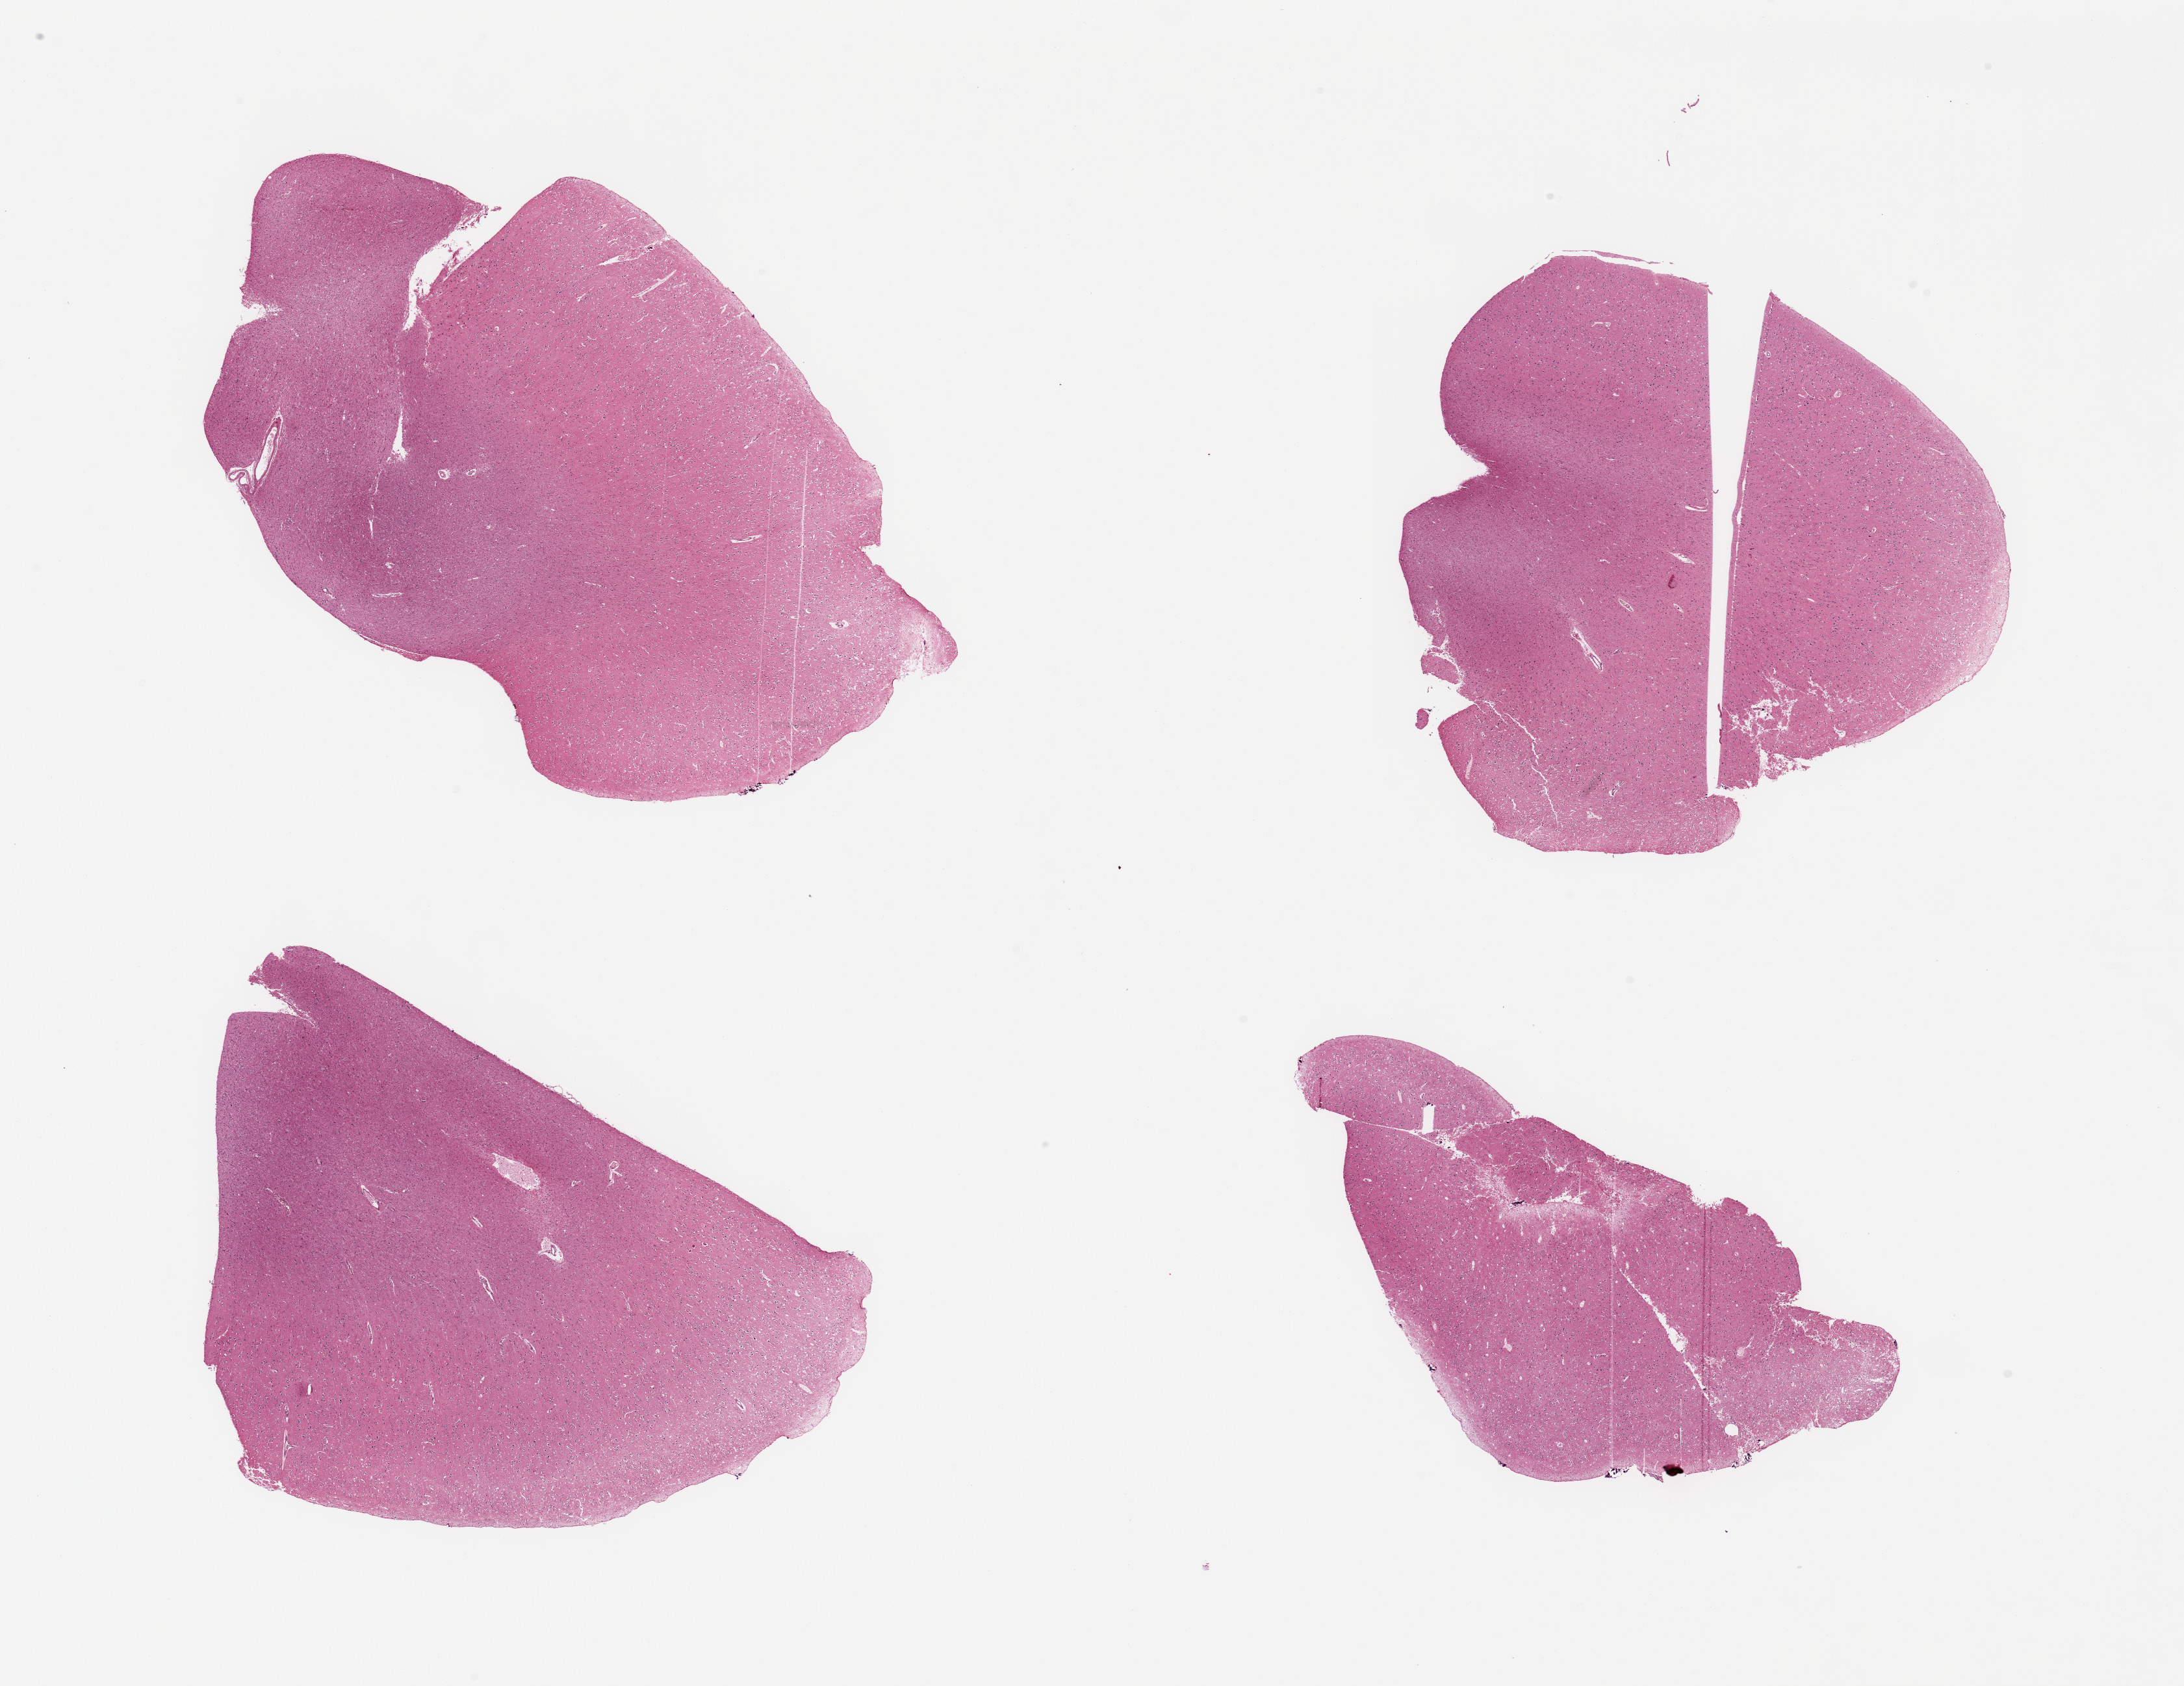
Whole-slide image, hematoxylin and eosin (H&E) stain, a low-resolution overview of the entire scanned area, about 26.6 x 20.5 mm; PAXgene-fixed paraffin-embedded (PFPE) section; section of cerebral cortex (target tissue); donor tissue sample.
Pathologist's review note for this sample: 4 pieces, no abnormalities.